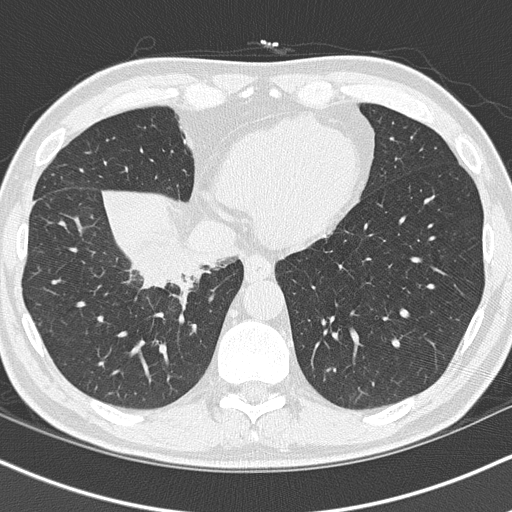
Axial slice from a low-dose chest CT screening exam; baseline screening round; lung window (W 1500 / L -600 HU); 2 mm slice thickness; lung (sharp) reconstruction kernel (B50f); 120 kVp; slice 34 of 151 in the series; 512 × 512 image matrix, field of view 320 × 320 mm. Male, age 55 years at enrolment. Current smoker at enrolment.
- Expert reader's lesion annotation, box from (x=114, y=220) to (x=246, y=321) px.
- The exam's reader record, not a measurement of the box and not confirmed to be the same lesion: non-calcified nodule or mass ≥4 mm, right lower lobe, 6 × 5 mm, spiculated (stellate) margins, soft tissue attenuation.